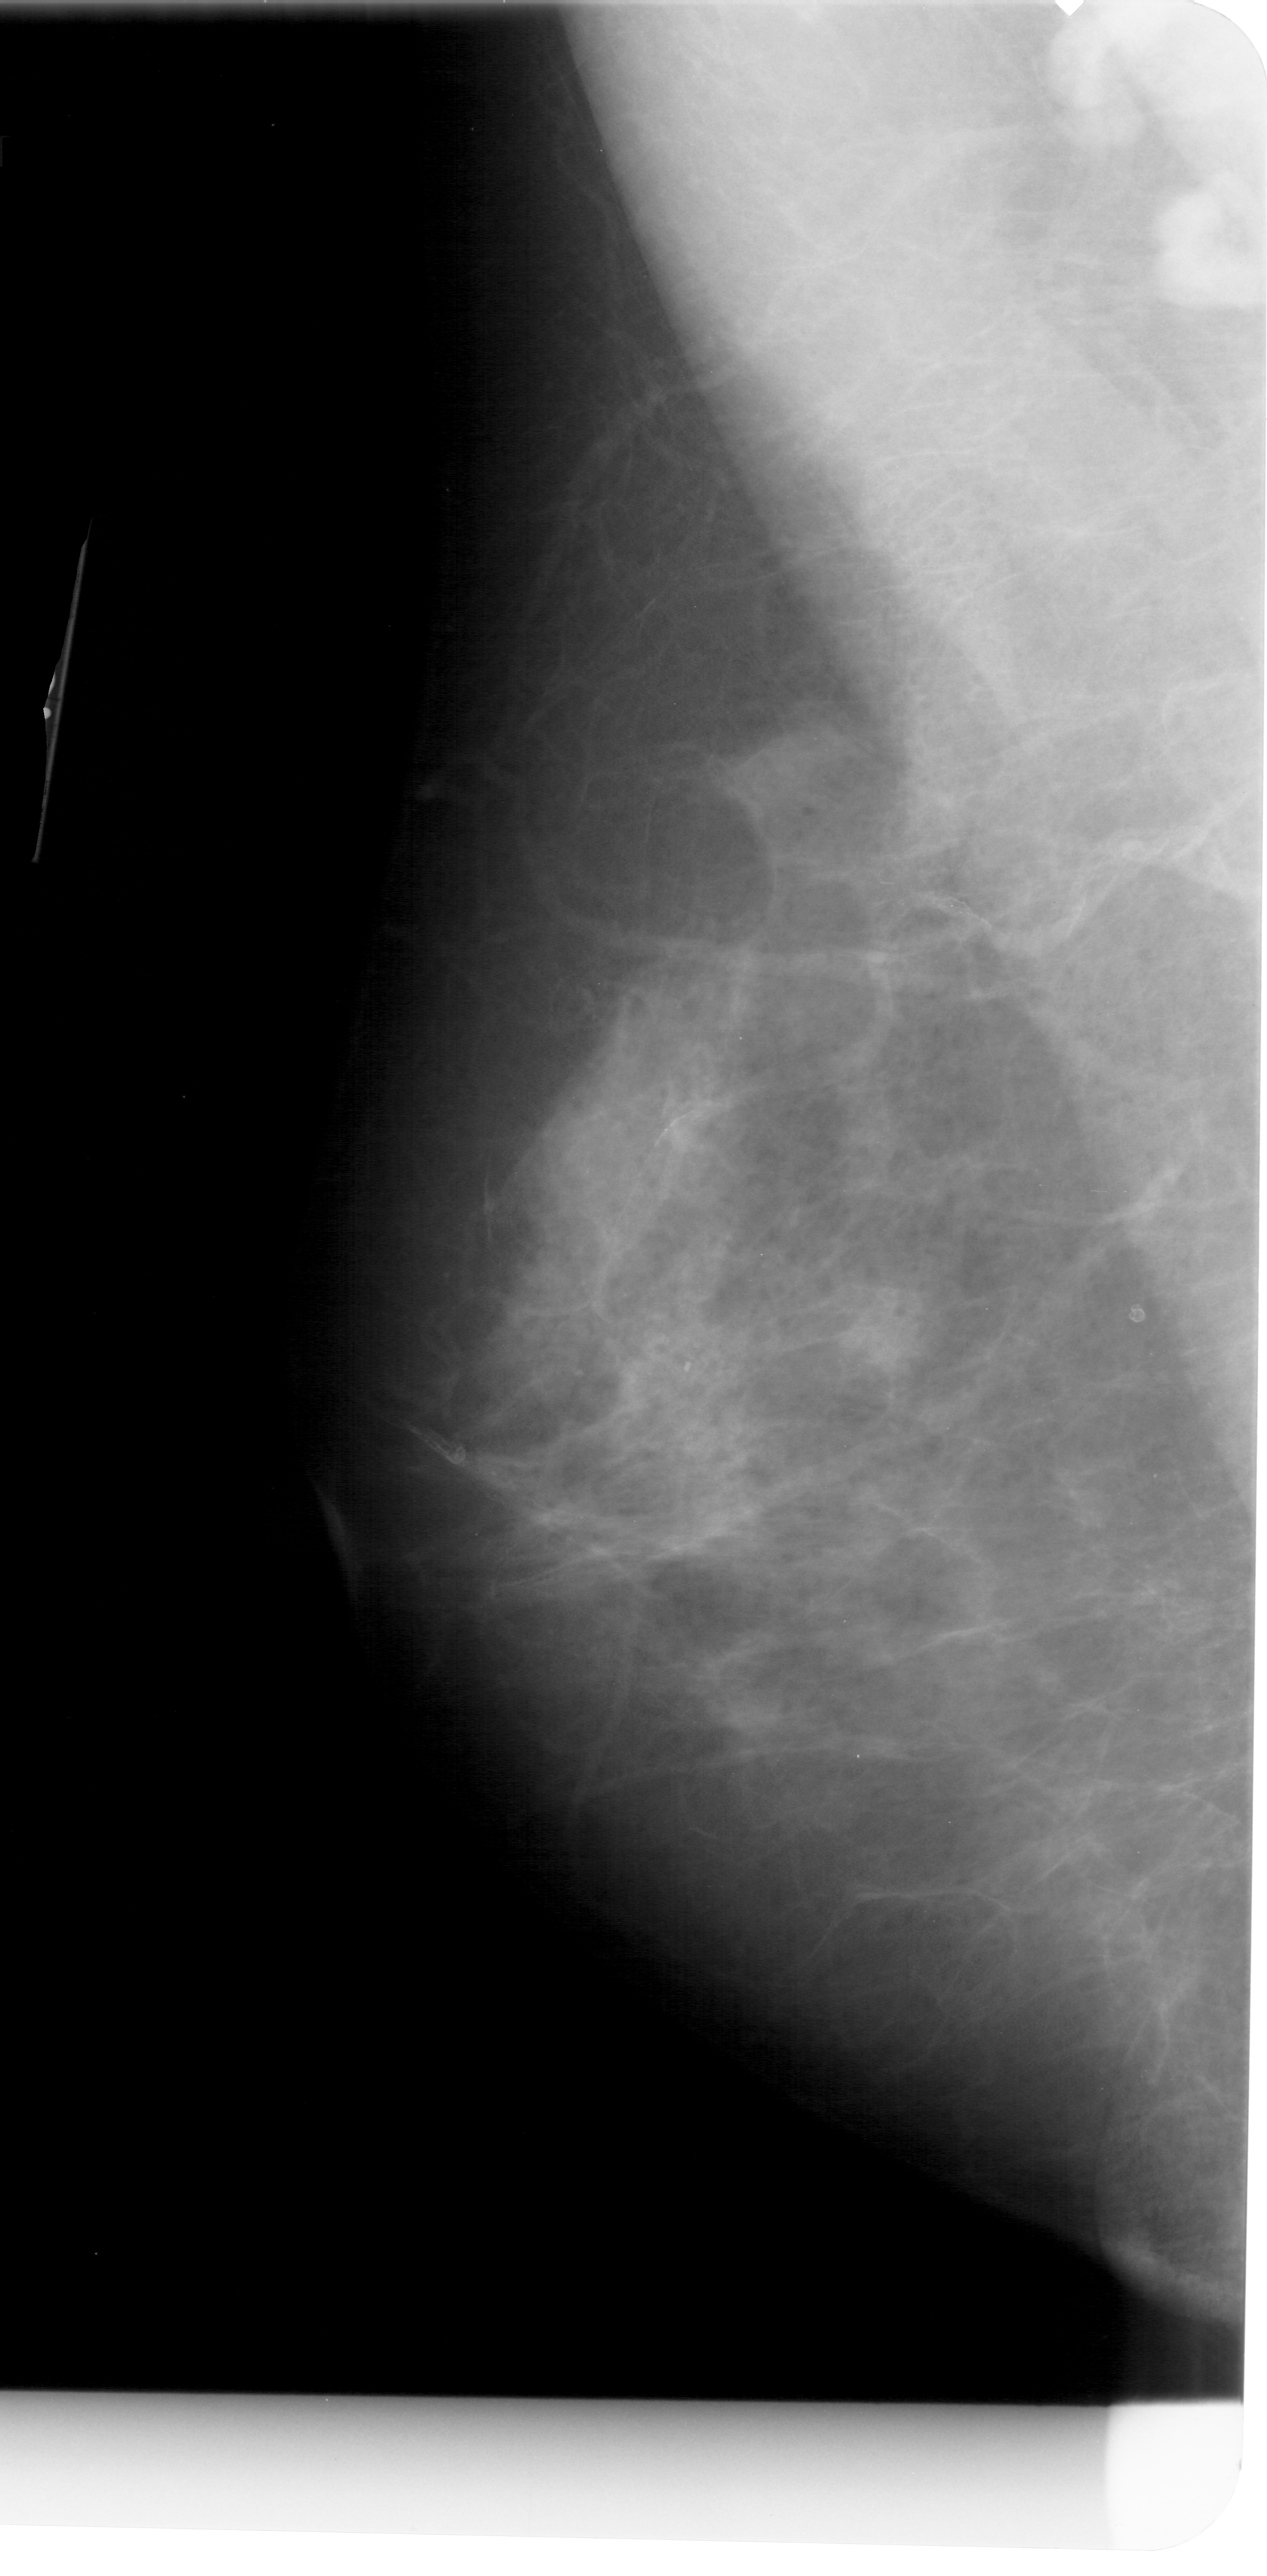
Digitized screen-film mammogram; left breast; MLO view; breast composition: extremely dense (BI-RADS density category 4 of 4); 1267 × 2576 image matrix.
Expert-marked regions of interest on this film, with their recorded descriptors:
- mass, shape irregular, margins ill defined; BI-RADS assessment category 4; subtlety rating 3 on a 1 (subtle) to 5 (obvious) scale; pathology (as recorded): benign: bounding box (x1, y1, x2, y2) in pixels: (831, 1271, 932, 1390)